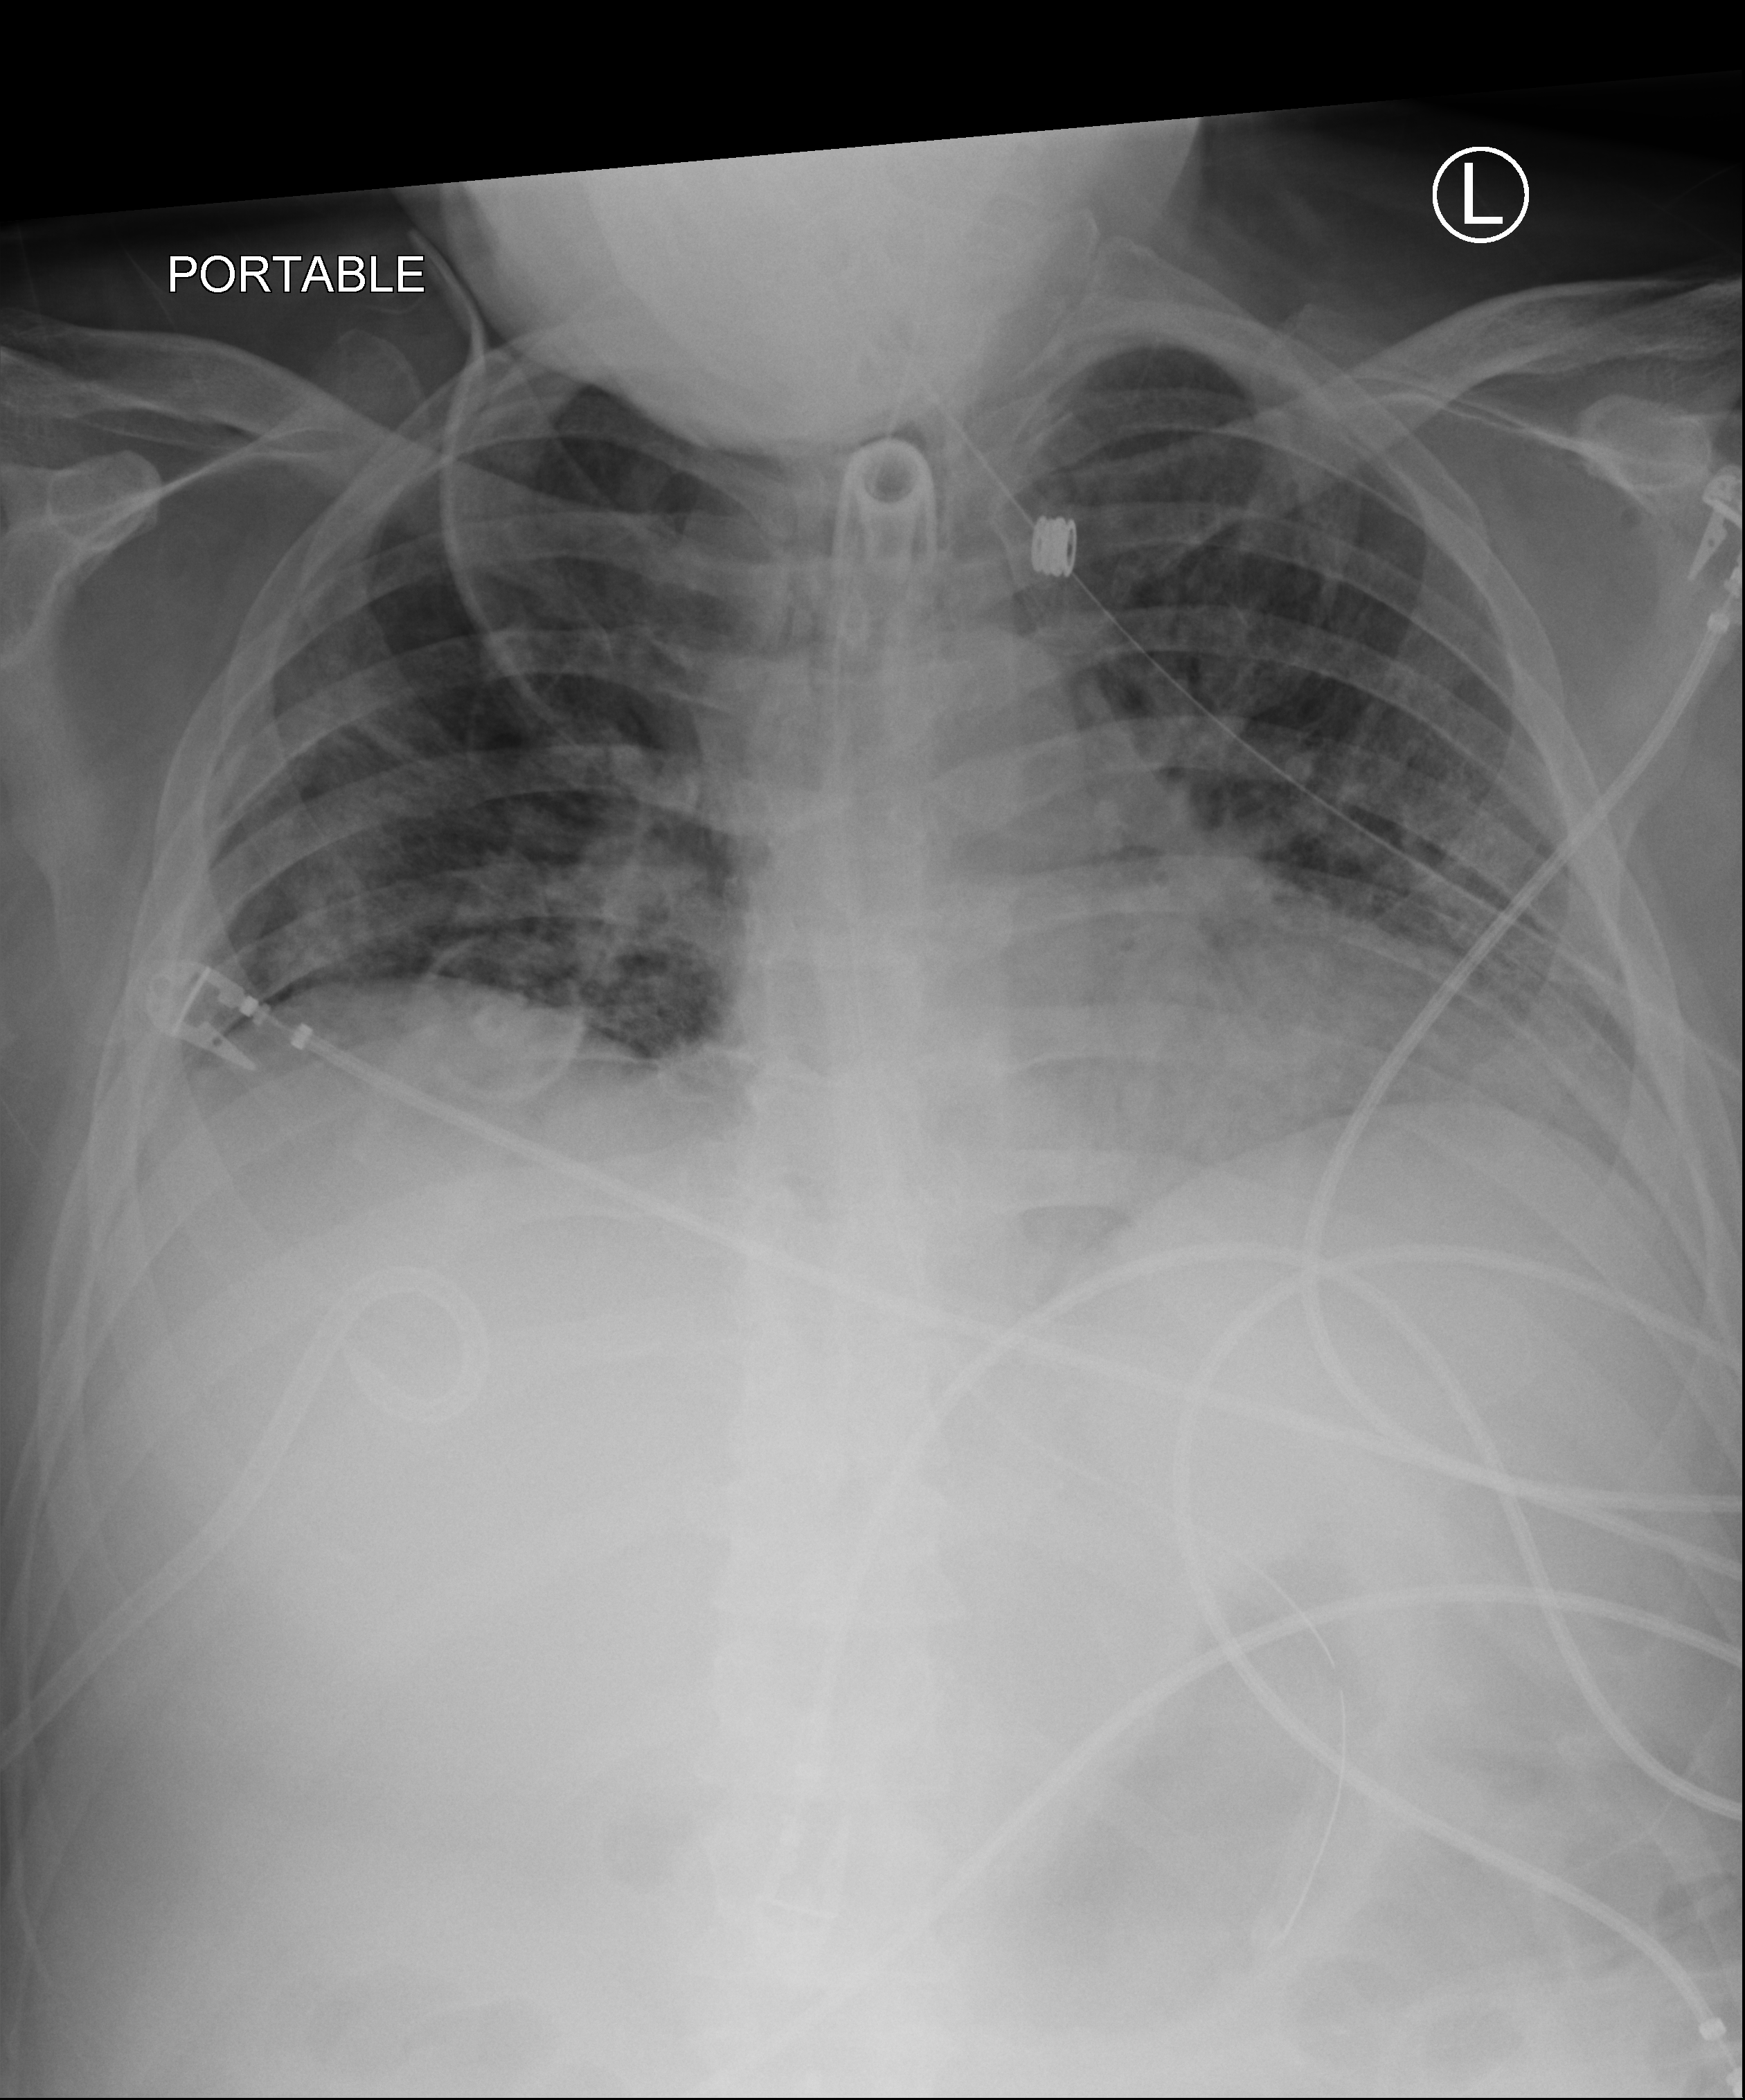
Portable chest radiograph, anteroposterior (AP) projection. Male patient hospitalised with COVID-19, age 18–59 years.
Hospital-stay facts (about this admission, not read from this image; timing relative to this image not recorded): admitted to intensive care during this hospital stay: yes.